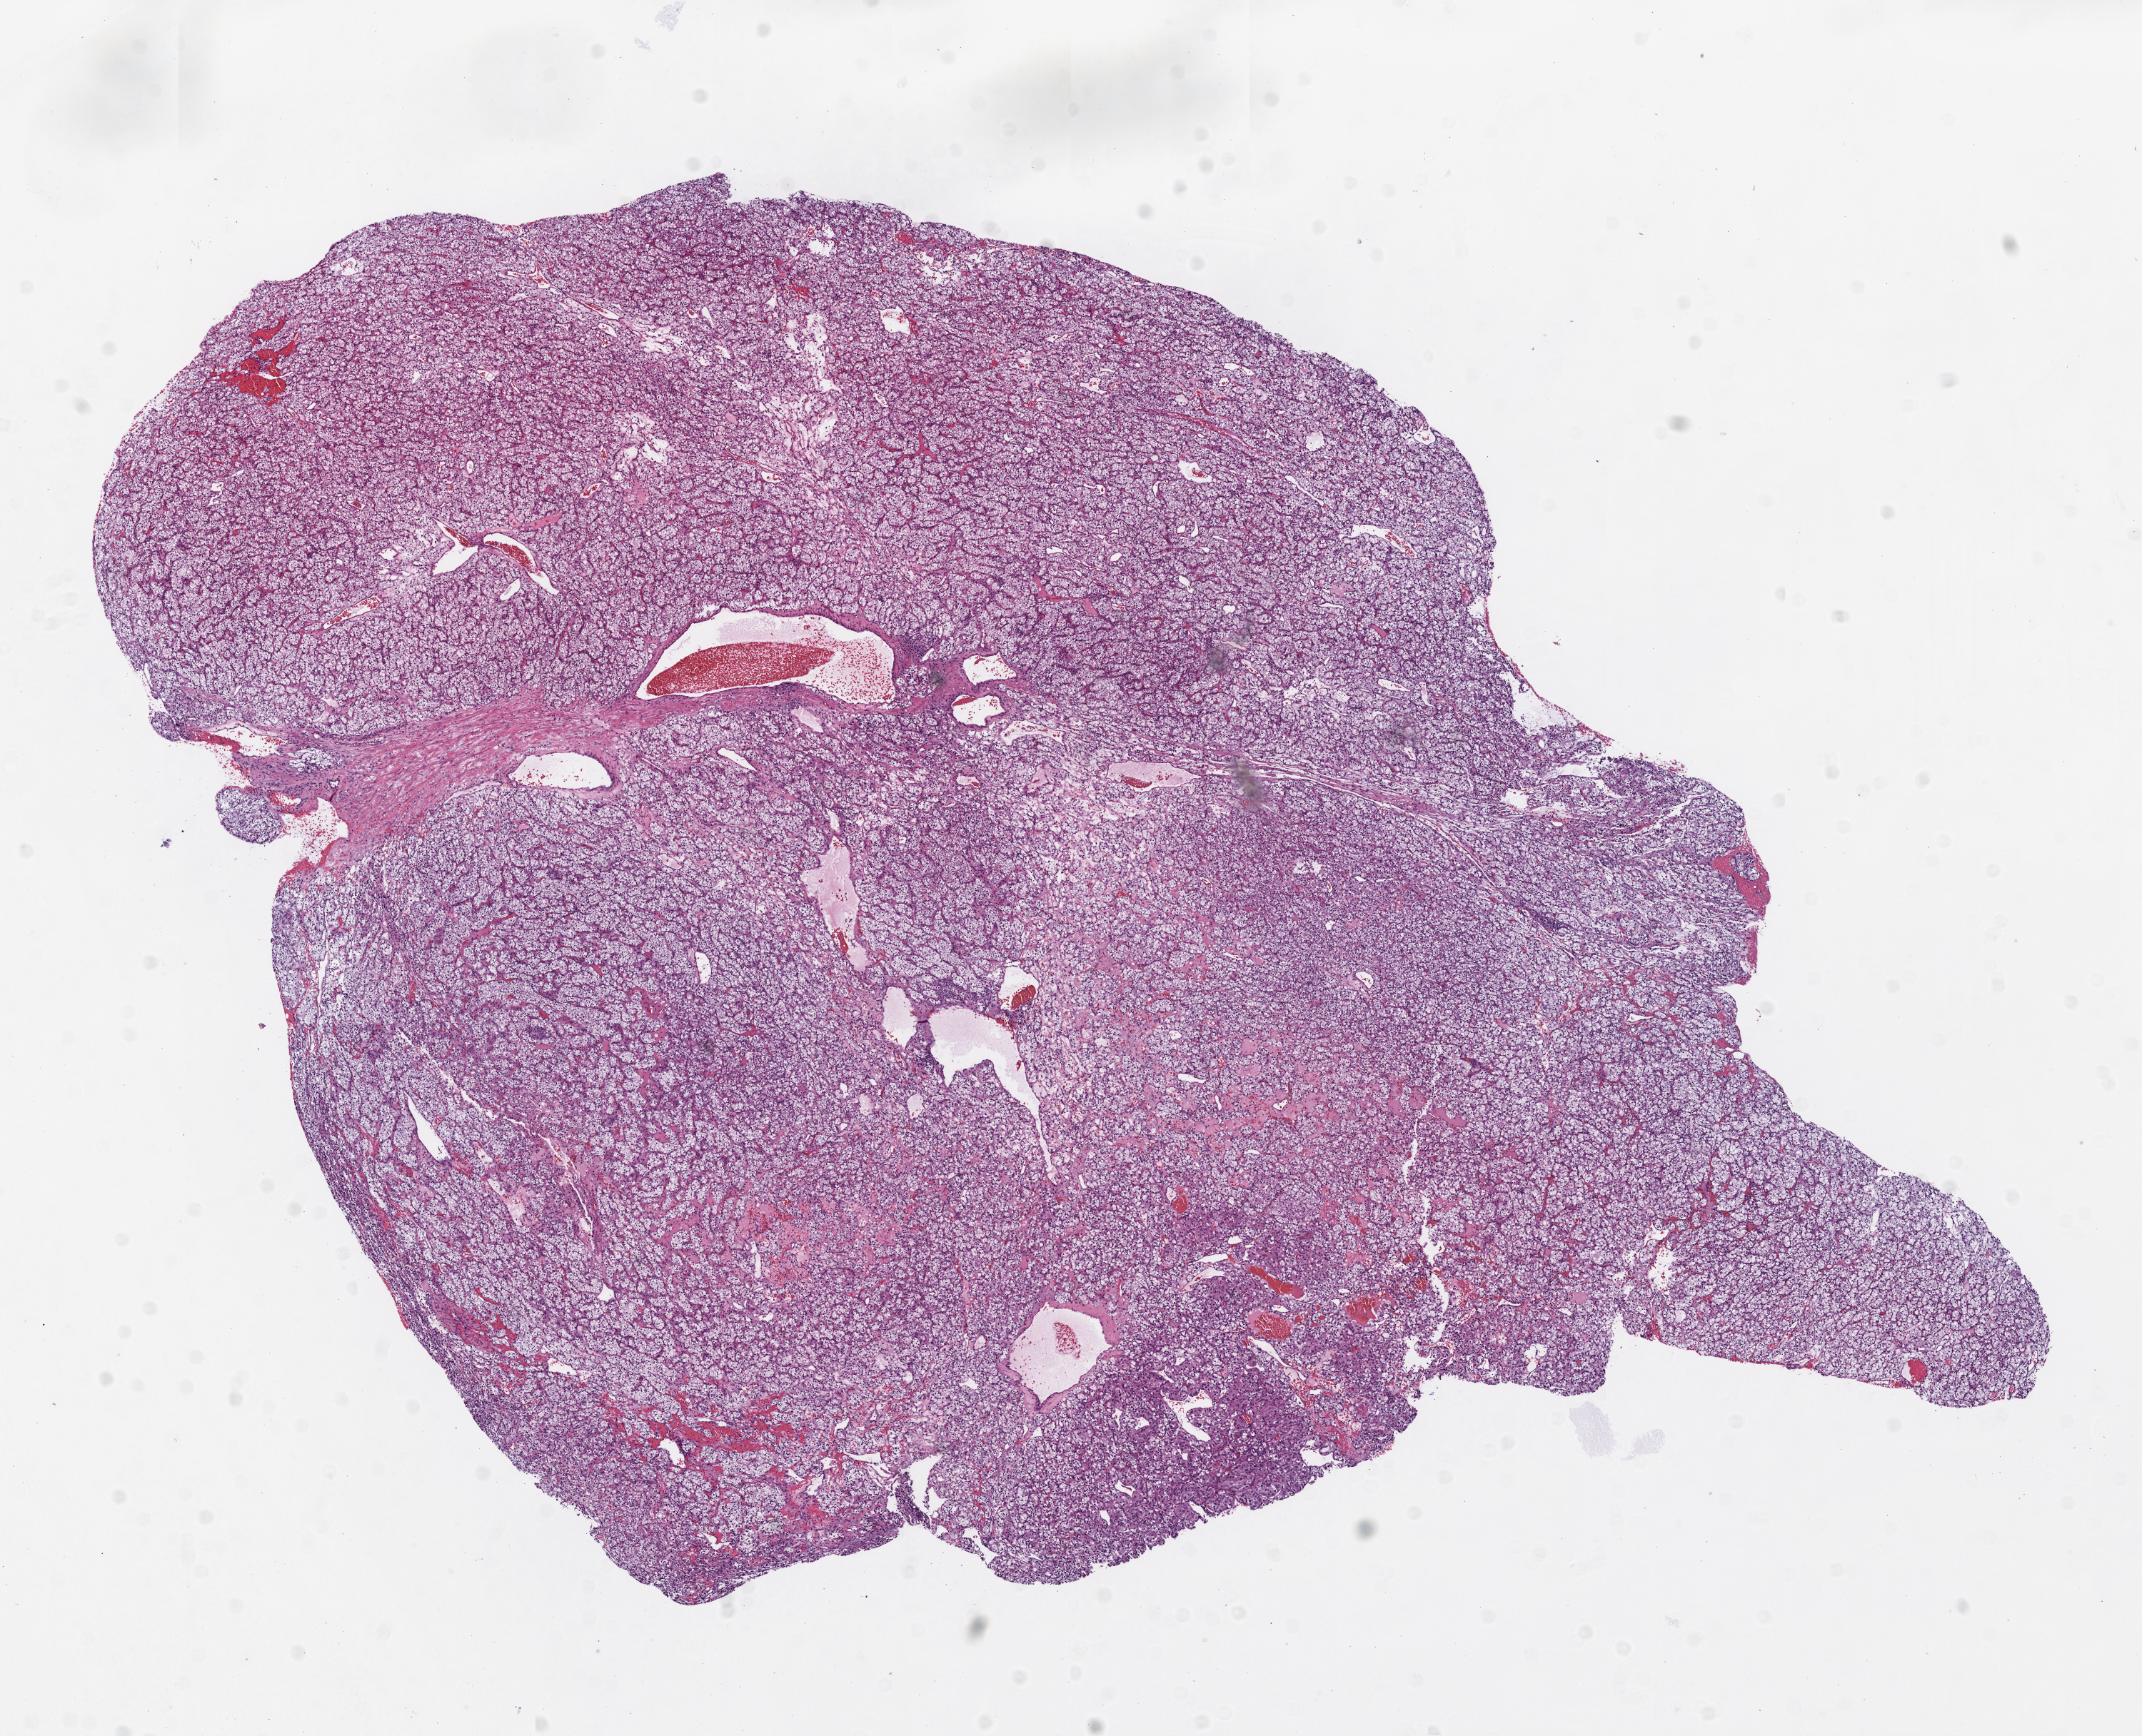
Digitized Hematoxylin and eosin (H&E) stained tissue section (whole slide) — a low-resolution overview of the entire scanned area, about 12.0 x 9.8 mm, frozen section, kidney, primary tumour sample. Male, age 73 years at initial diagnosis. Histologic grade: G2 (moderately differentiated). Pathologist review of this section (percent, as recorded): tumour cells 95%, tumour nuclei 90%, normal cells 0%, stromal cells 5%, necrosis 0%.
AJCC pathologic stage: I. Pathologic diagnosis: Clear cell adenocarcinoma, NOS. TNM: T1b NX M0.